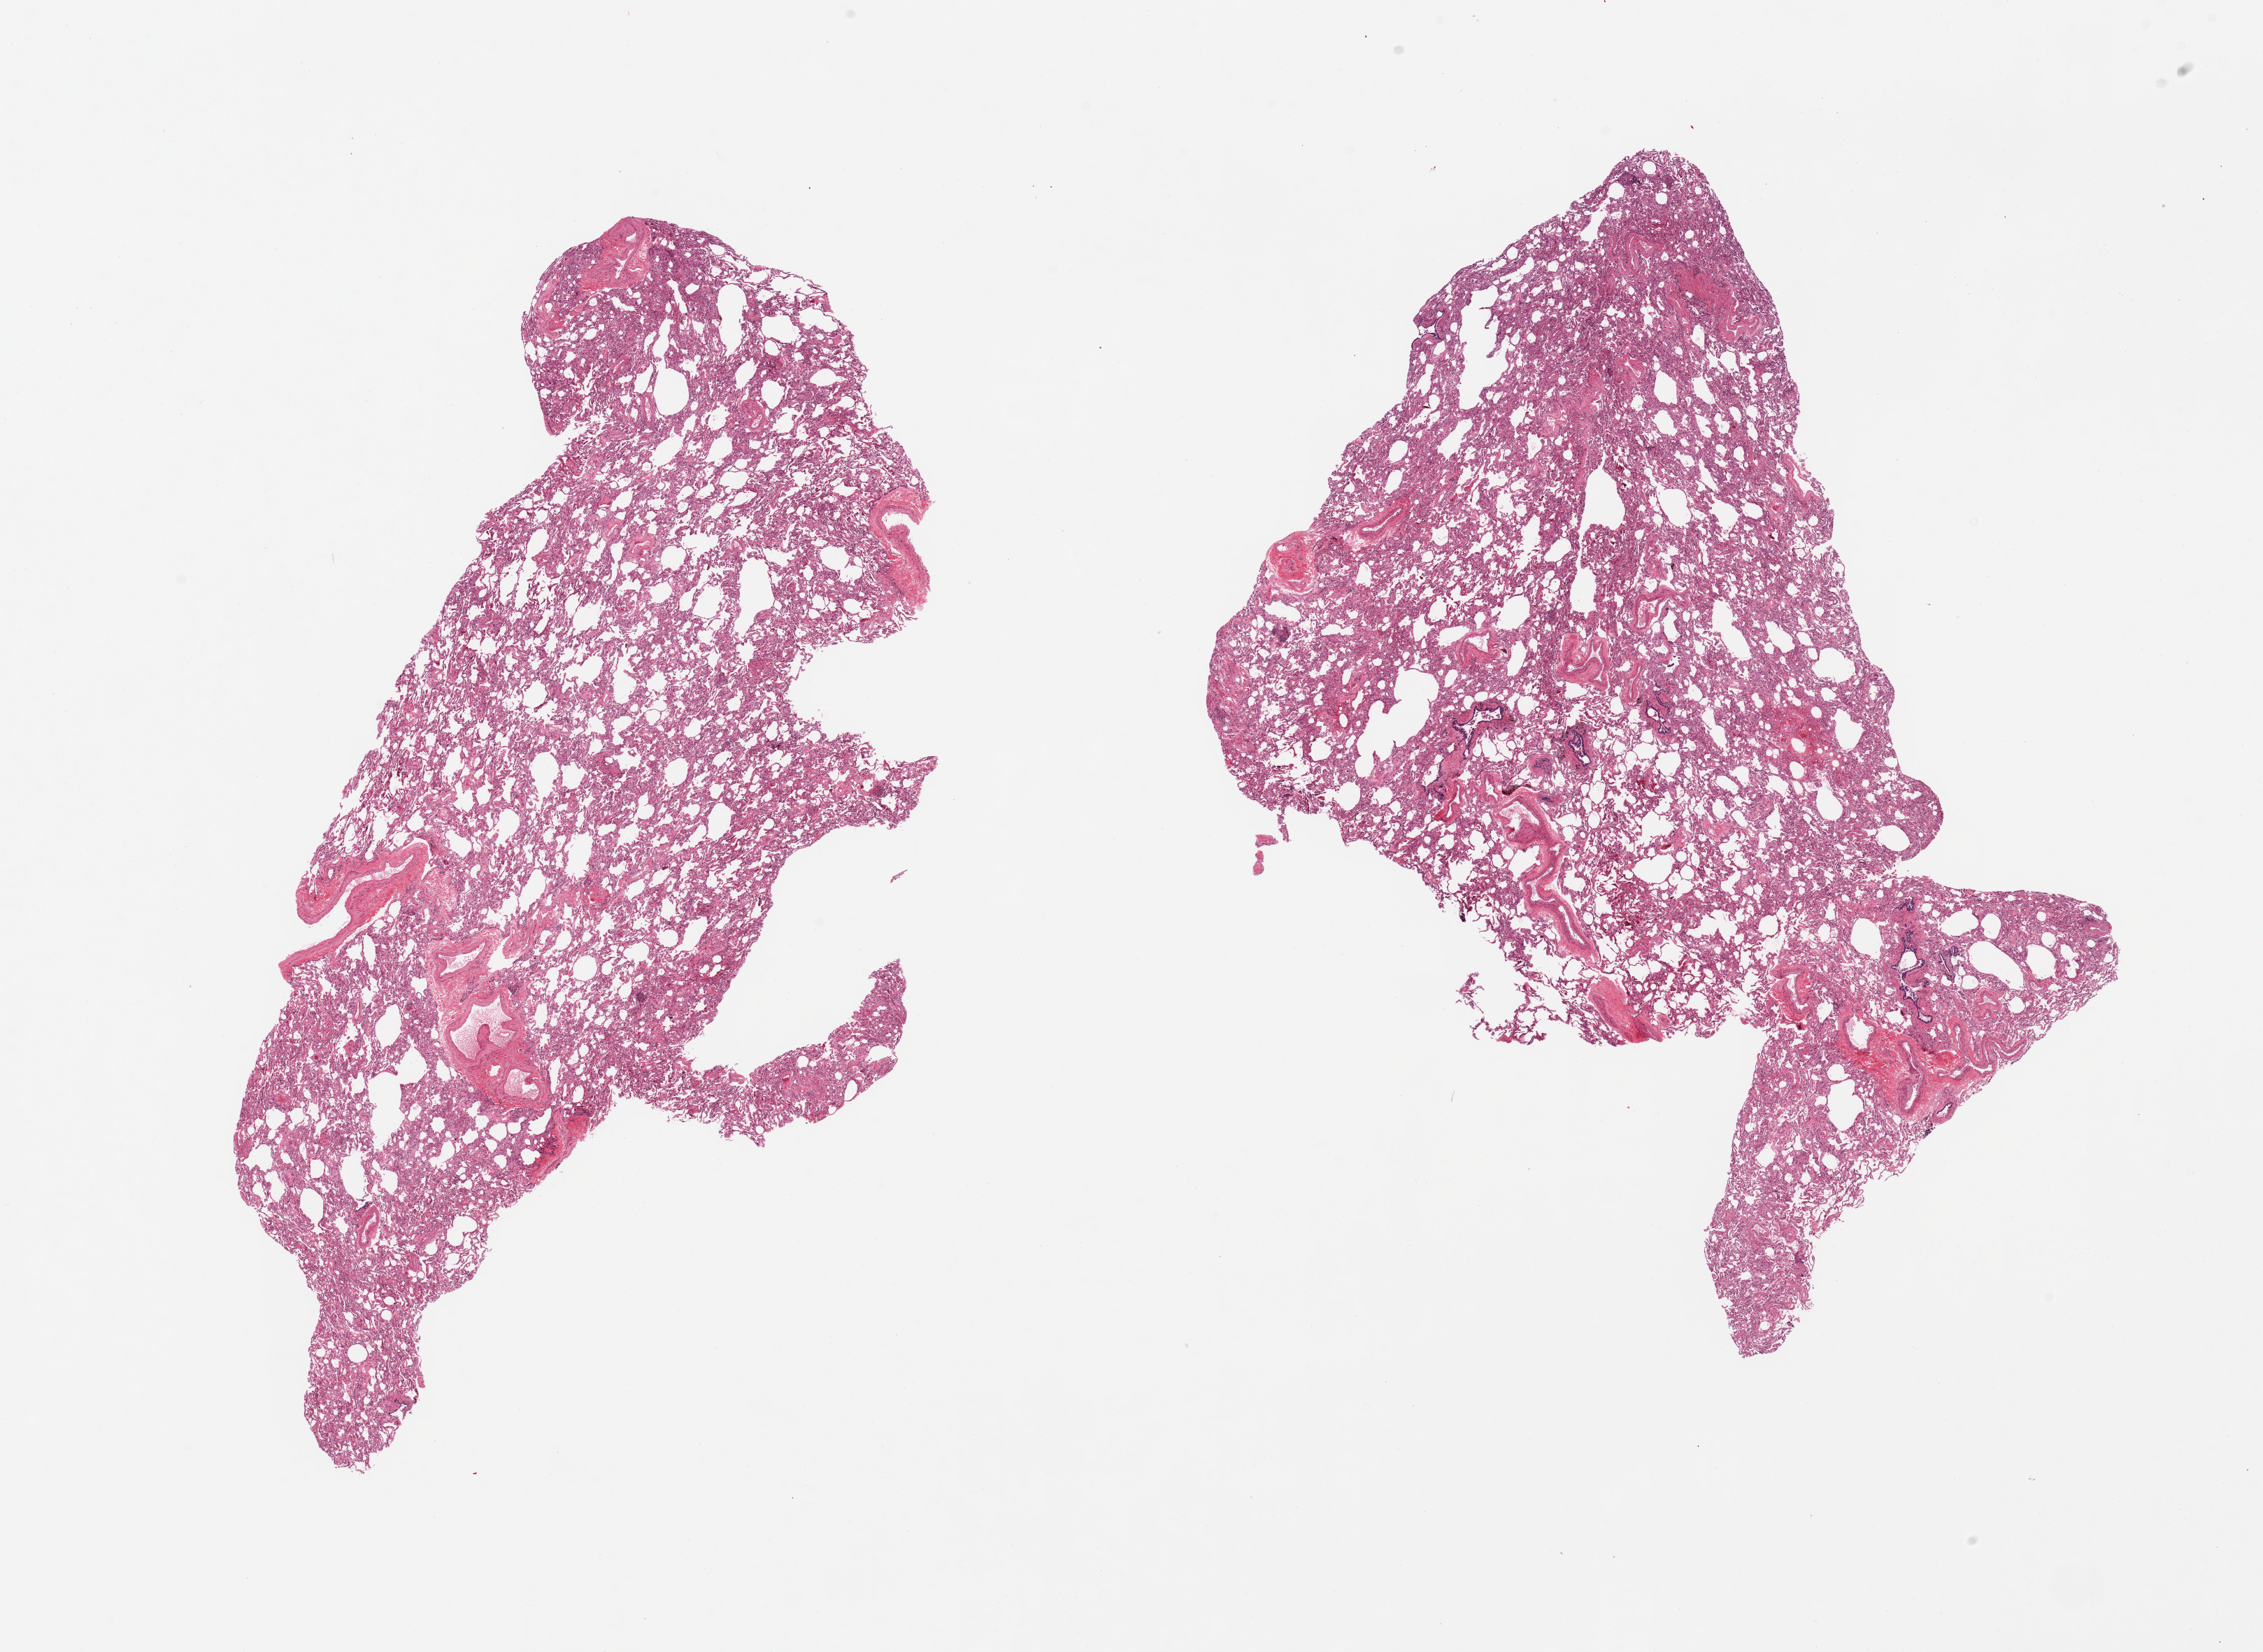
Haematoxylin and eosin whole-slide image, brightfield — low-resolution overview of the scanned area, about 25.6 x 18.7 mm; PAXgene-fixed, paraffin-embedded tissue; sampled site (target tissue): lung; tissue donor sample. Female donor.
Review note (as recorded): 2 pieces, patchy bronchopneumonia.